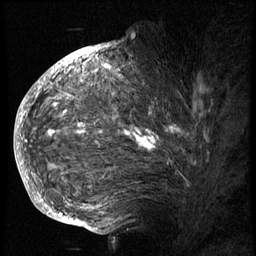
Breast MRI (dynamic contrast-enhanced), one sagittal slice. Slice 44 of 74 in the series (ordered by position). 3 images stored at this slice position (order not interpretable as contrast timing). 1.5 T. TE 4.2 ms, TR 8.9 ms. 2.5 mm slice thickness. 256 × 256 image matrix, field of view 200 × 200 mm. Patient: female, 57 years. From the clinical record (not read from this slice): setting: breast cancer imaged before/during neoadjuvant chemotherapy; receptor status: HER2-positive.
Structures marked on this image (semi-automatic segmentation, software-assisted and operator-edited):
- analysis volume of interest (the breast-tissue region the enhancement analysis was run in; not a lesion): box from (x=40, y=62) to (x=242, y=175) px
- tumour enhancement mask (voxels above the 140 % enhancement threshold inside the analysis volume of interest): (x=48, y=65)–(x=196, y=150)